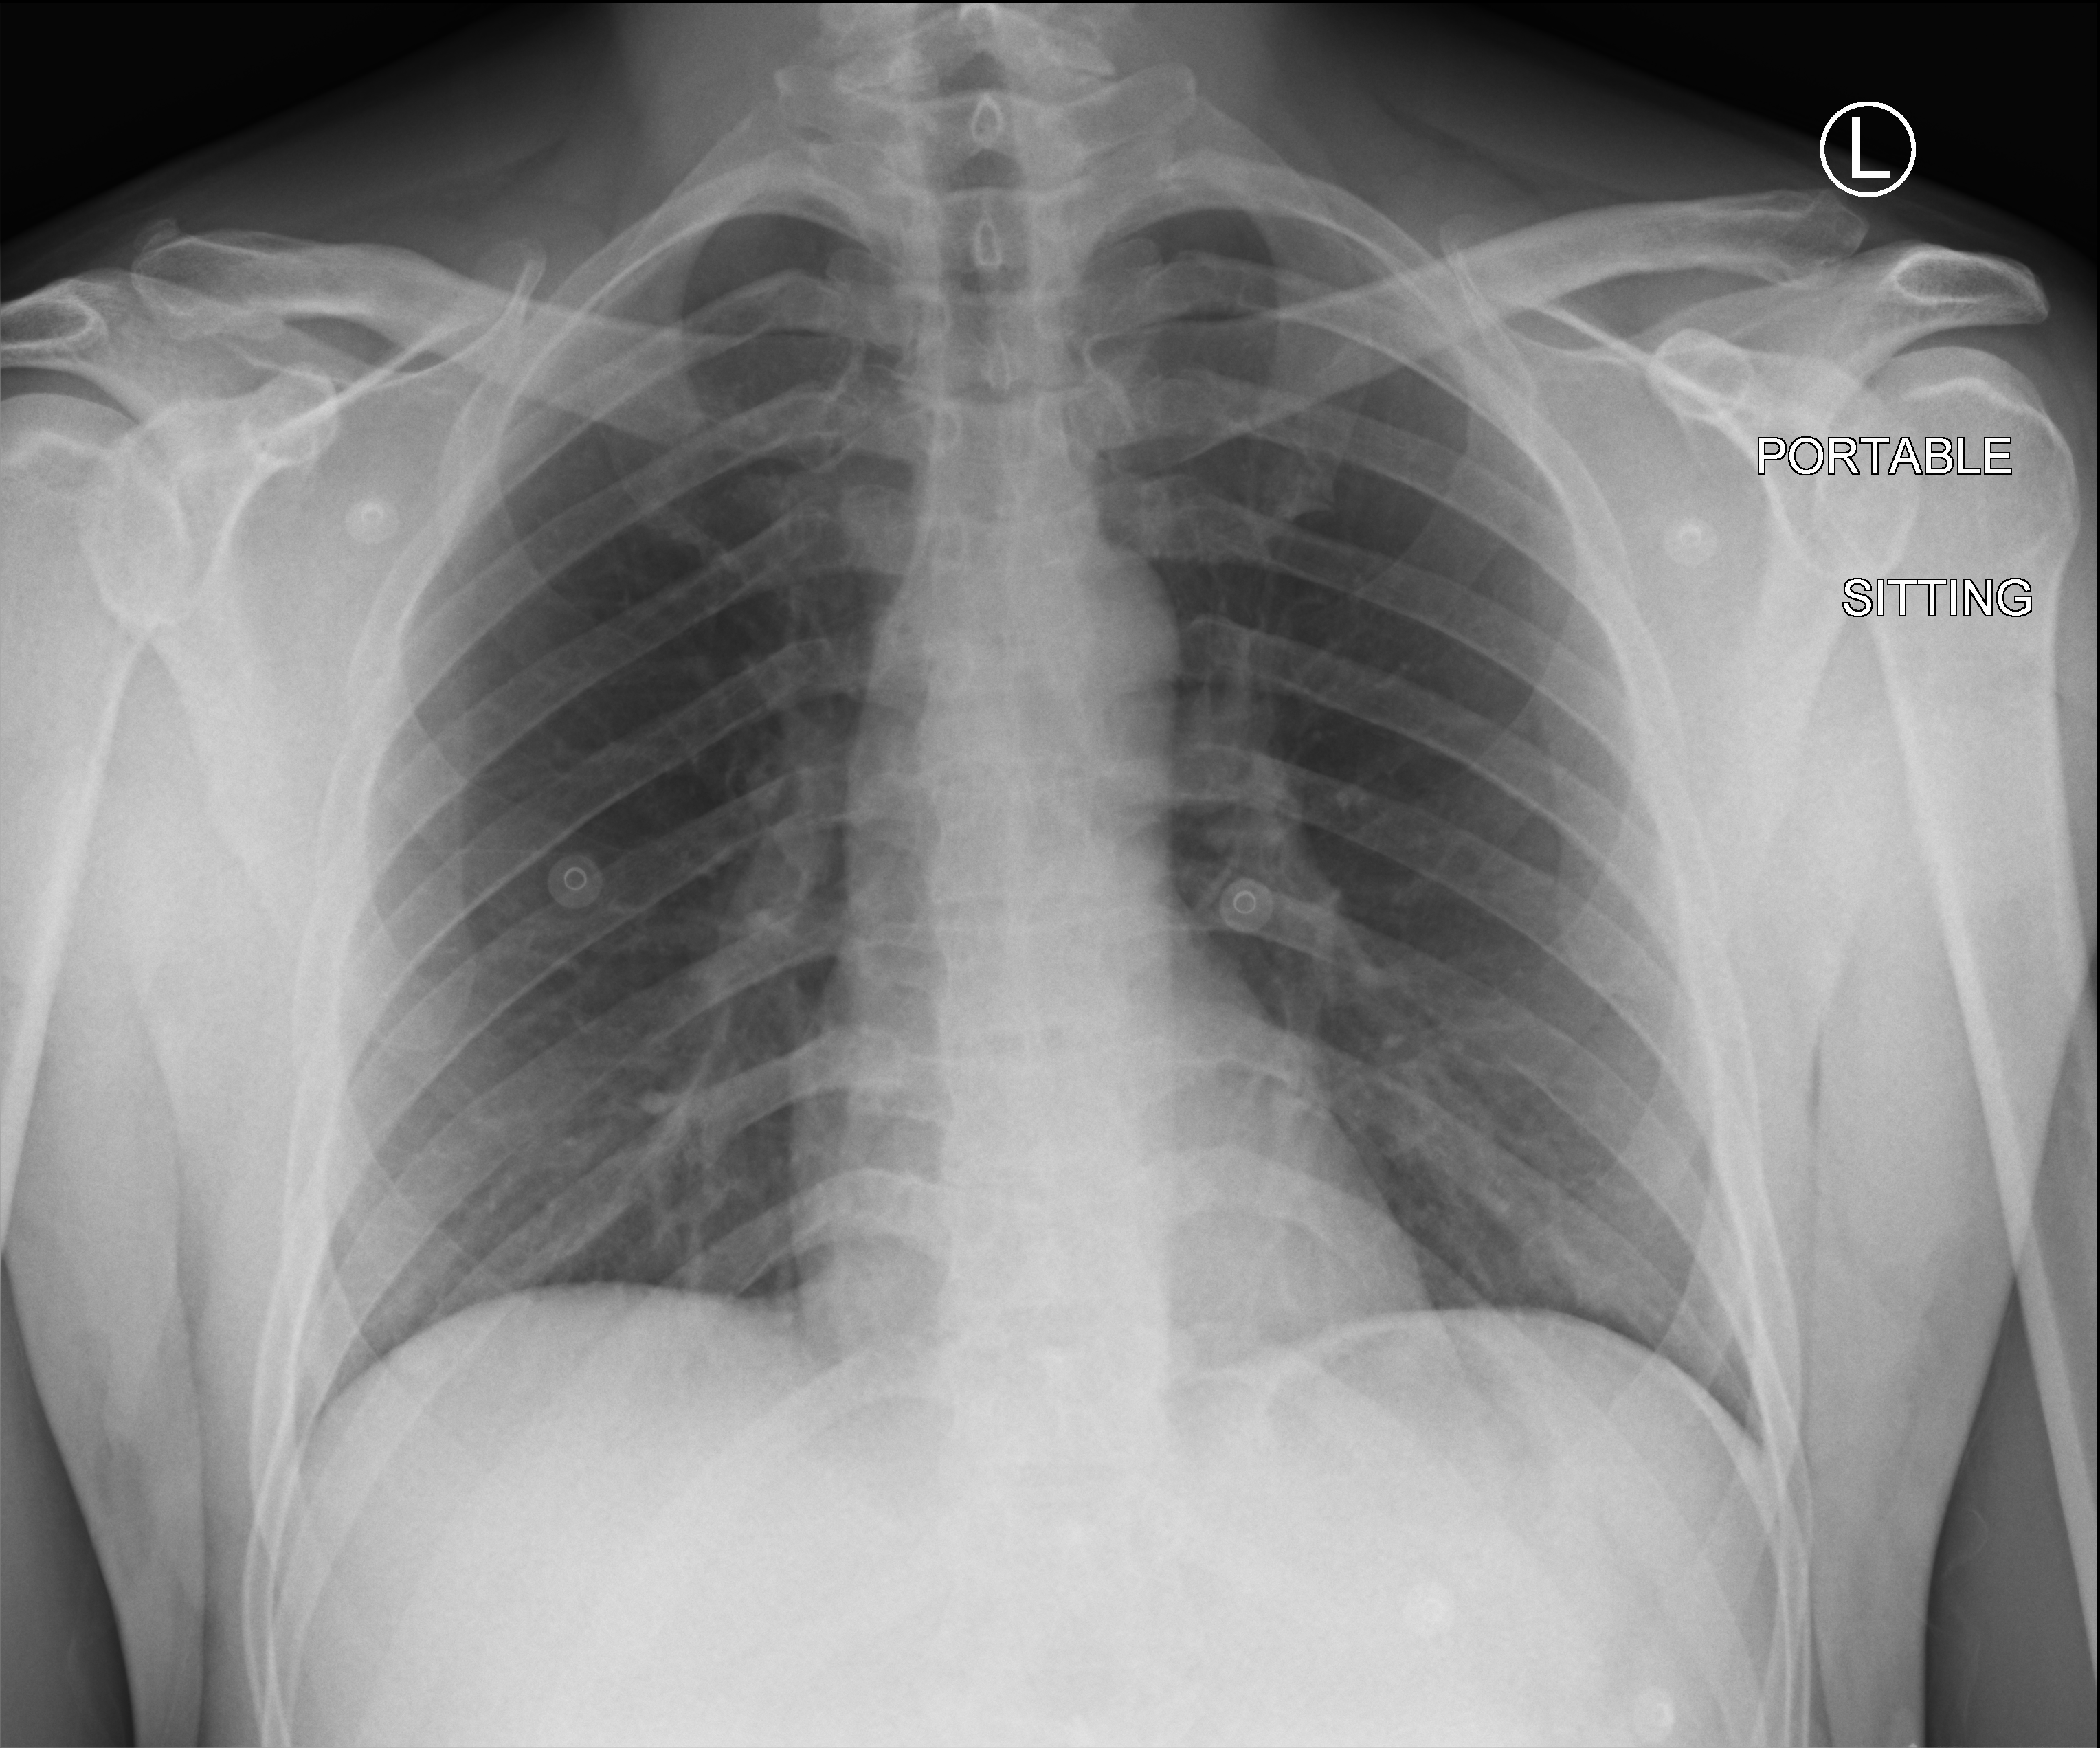
Bedside chest radiograph (computed radiography), anteroposterior (AP) projection. Patient hospitalised with COVID-19; male, aged 18–59 years.
Hospital-stay facts (about this admission, not read from this image; timing relative to this image not recorded): admitted to intensive care during this hospital stay: no; hypertension (admission record): no.